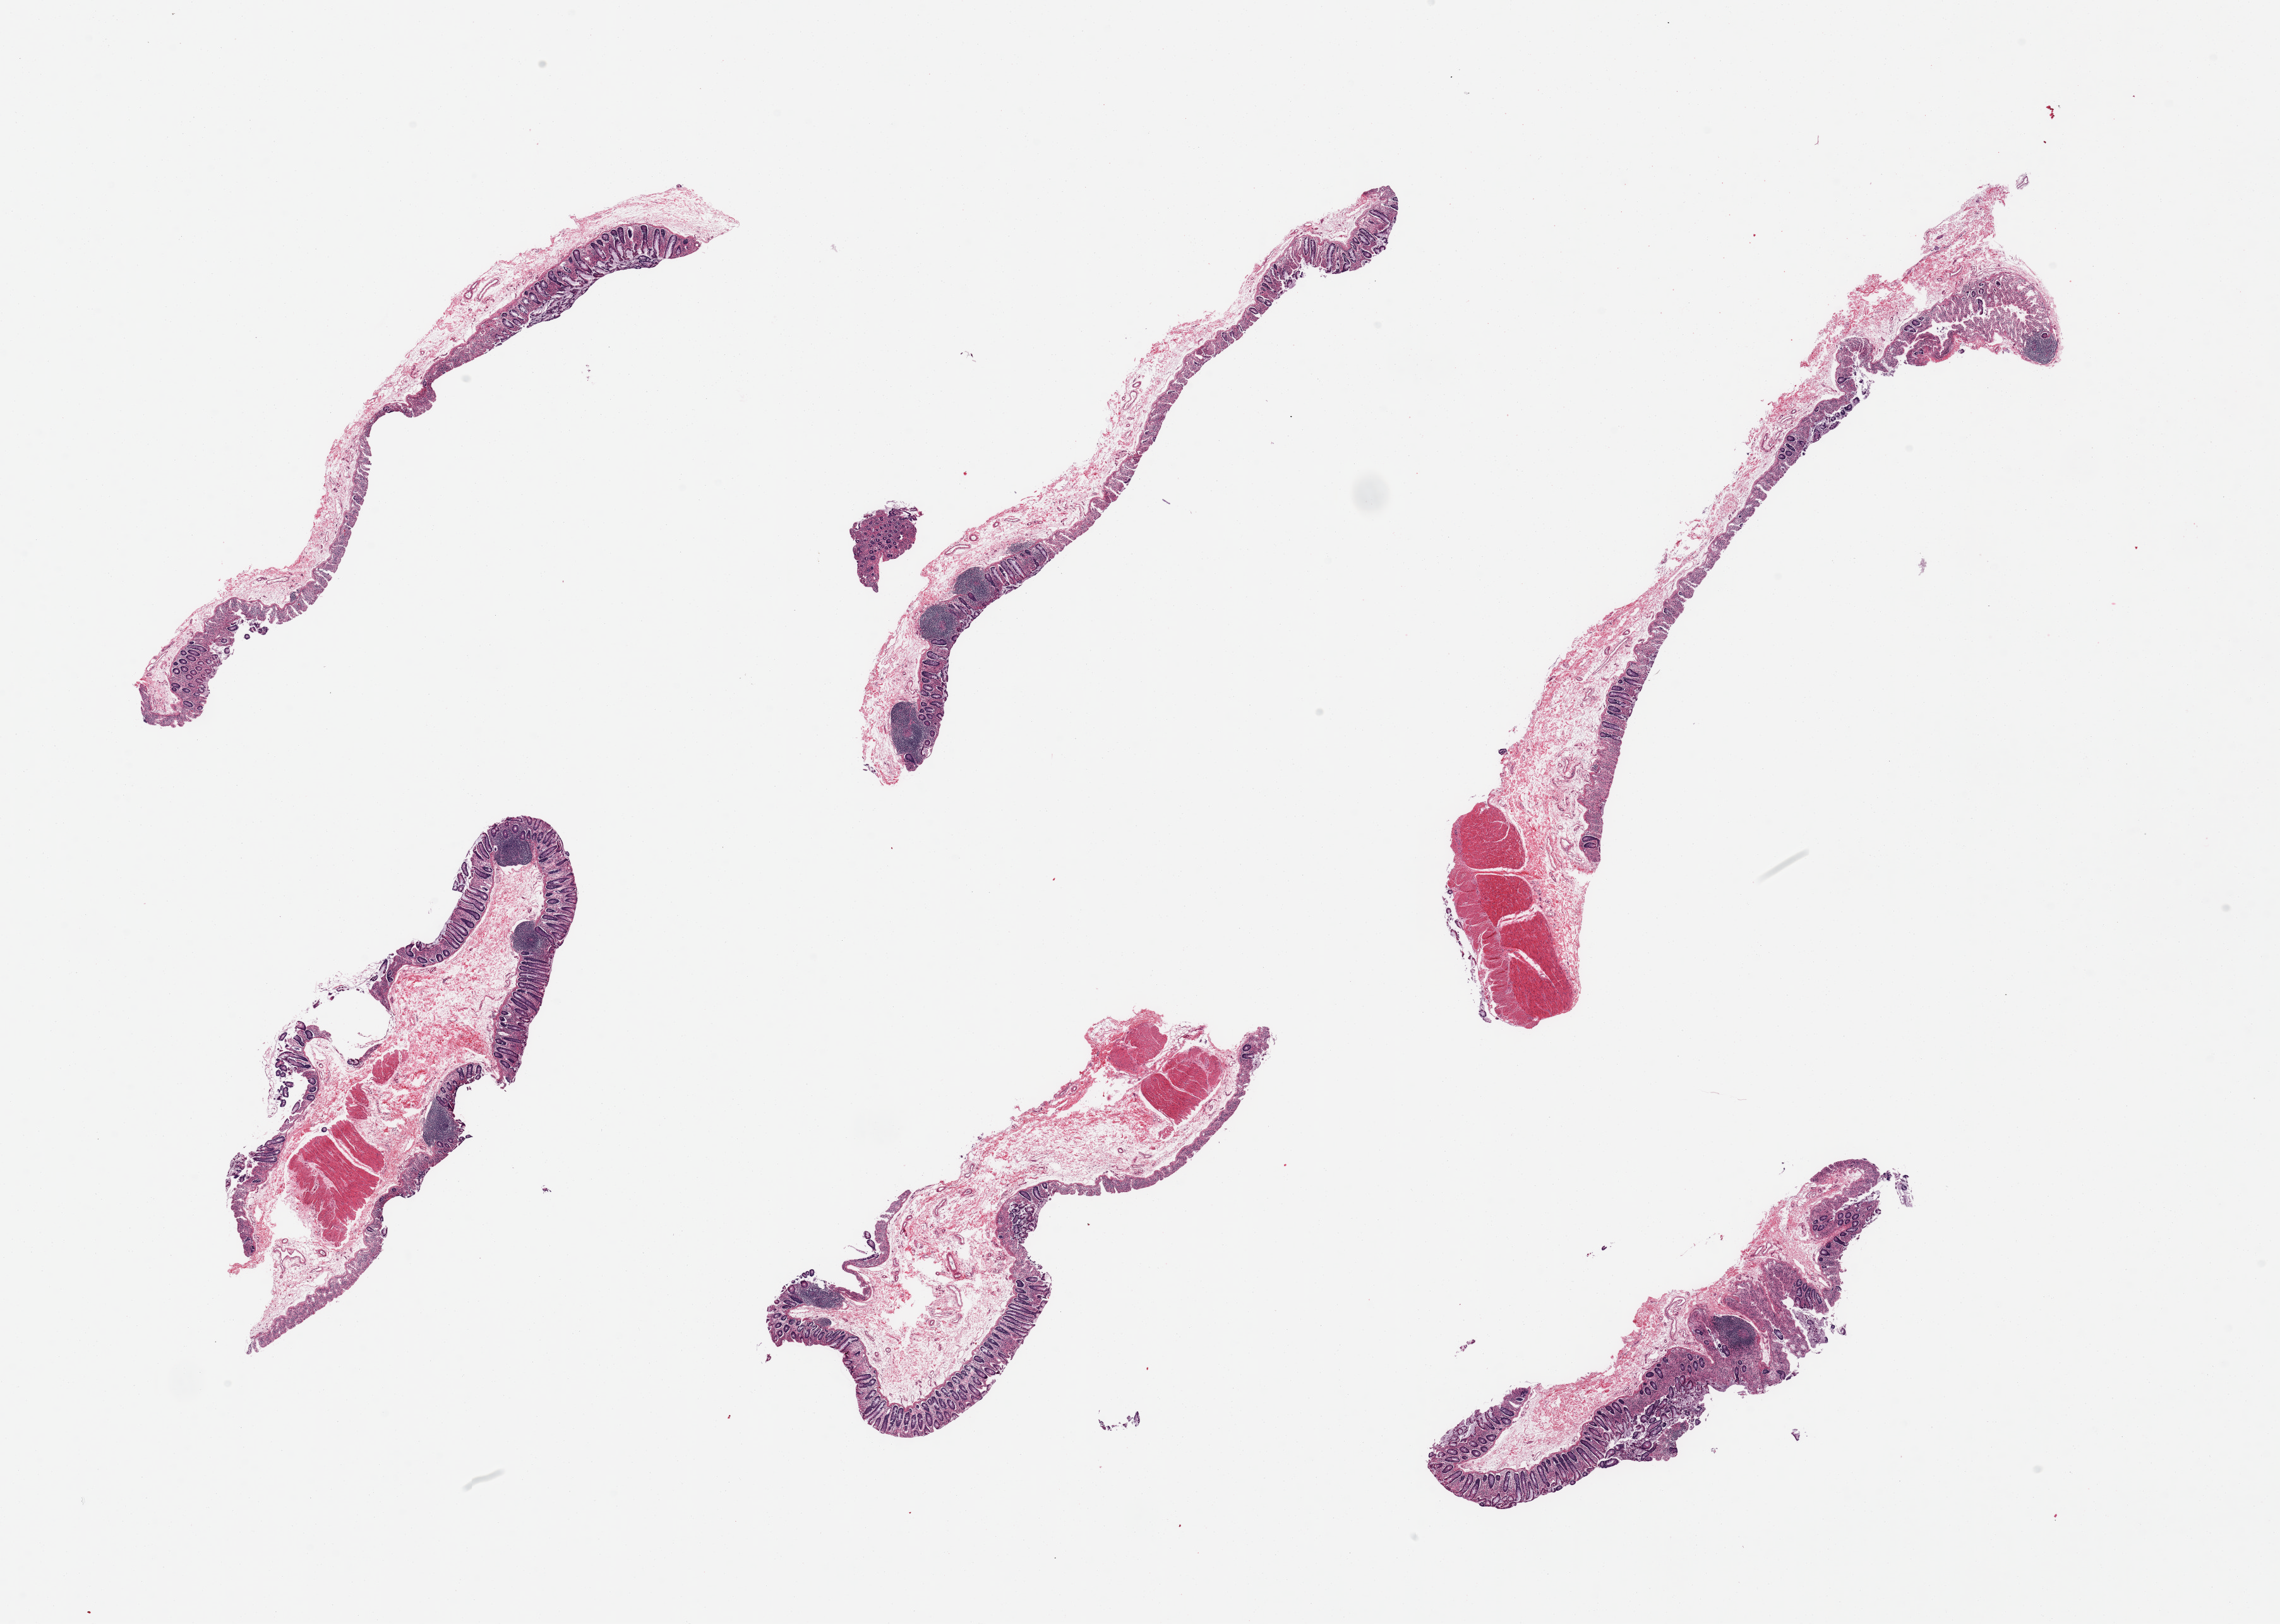
H&E whole-slide image — a low-resolution overview of the entire scanned area, about 28.5 x 20.3 mm (acquisition: 20x scan), PAXgene-fixed paraffin-embedded (PFPE) section, target tissue: transverse colon, donor tissue sample. Female donor.
Pathologist's review note for this sample: 6 pieces; grade 1 to 2 autolysed colonic mucosa; irregularly distributed lymphoid aggregates; 3 of 6 samples contain muscularis.